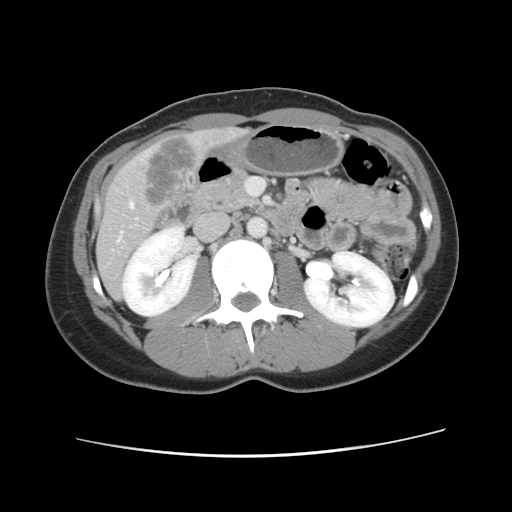
Contrast-enhanced abdominal CT, one axial slice. Intravenous contrast given. Soft-tissue window (W 400 / L 40 HU). 2.5 mm slice thickness. 512 × 512 image matrix, field of view 339 × 339 mm. Female patient, age 33 years. Case-level facts recorded for this patient, not image findings: diagnosis: colorectal cancer liver metastases, imaged before liver resection.
Structures marked on this image (expert manual segmentation):
- hepatic veins: box from (x=118, y=202) to (x=134, y=242) px
- liver: (x=97, y=128)–(x=243, y=298)
- planned liver remnant (the part of the liver to remain after resection): (x=97, y=241)–(x=127, y=297)
- liver metastasis: (x=144, y=137)–(x=196, y=207)